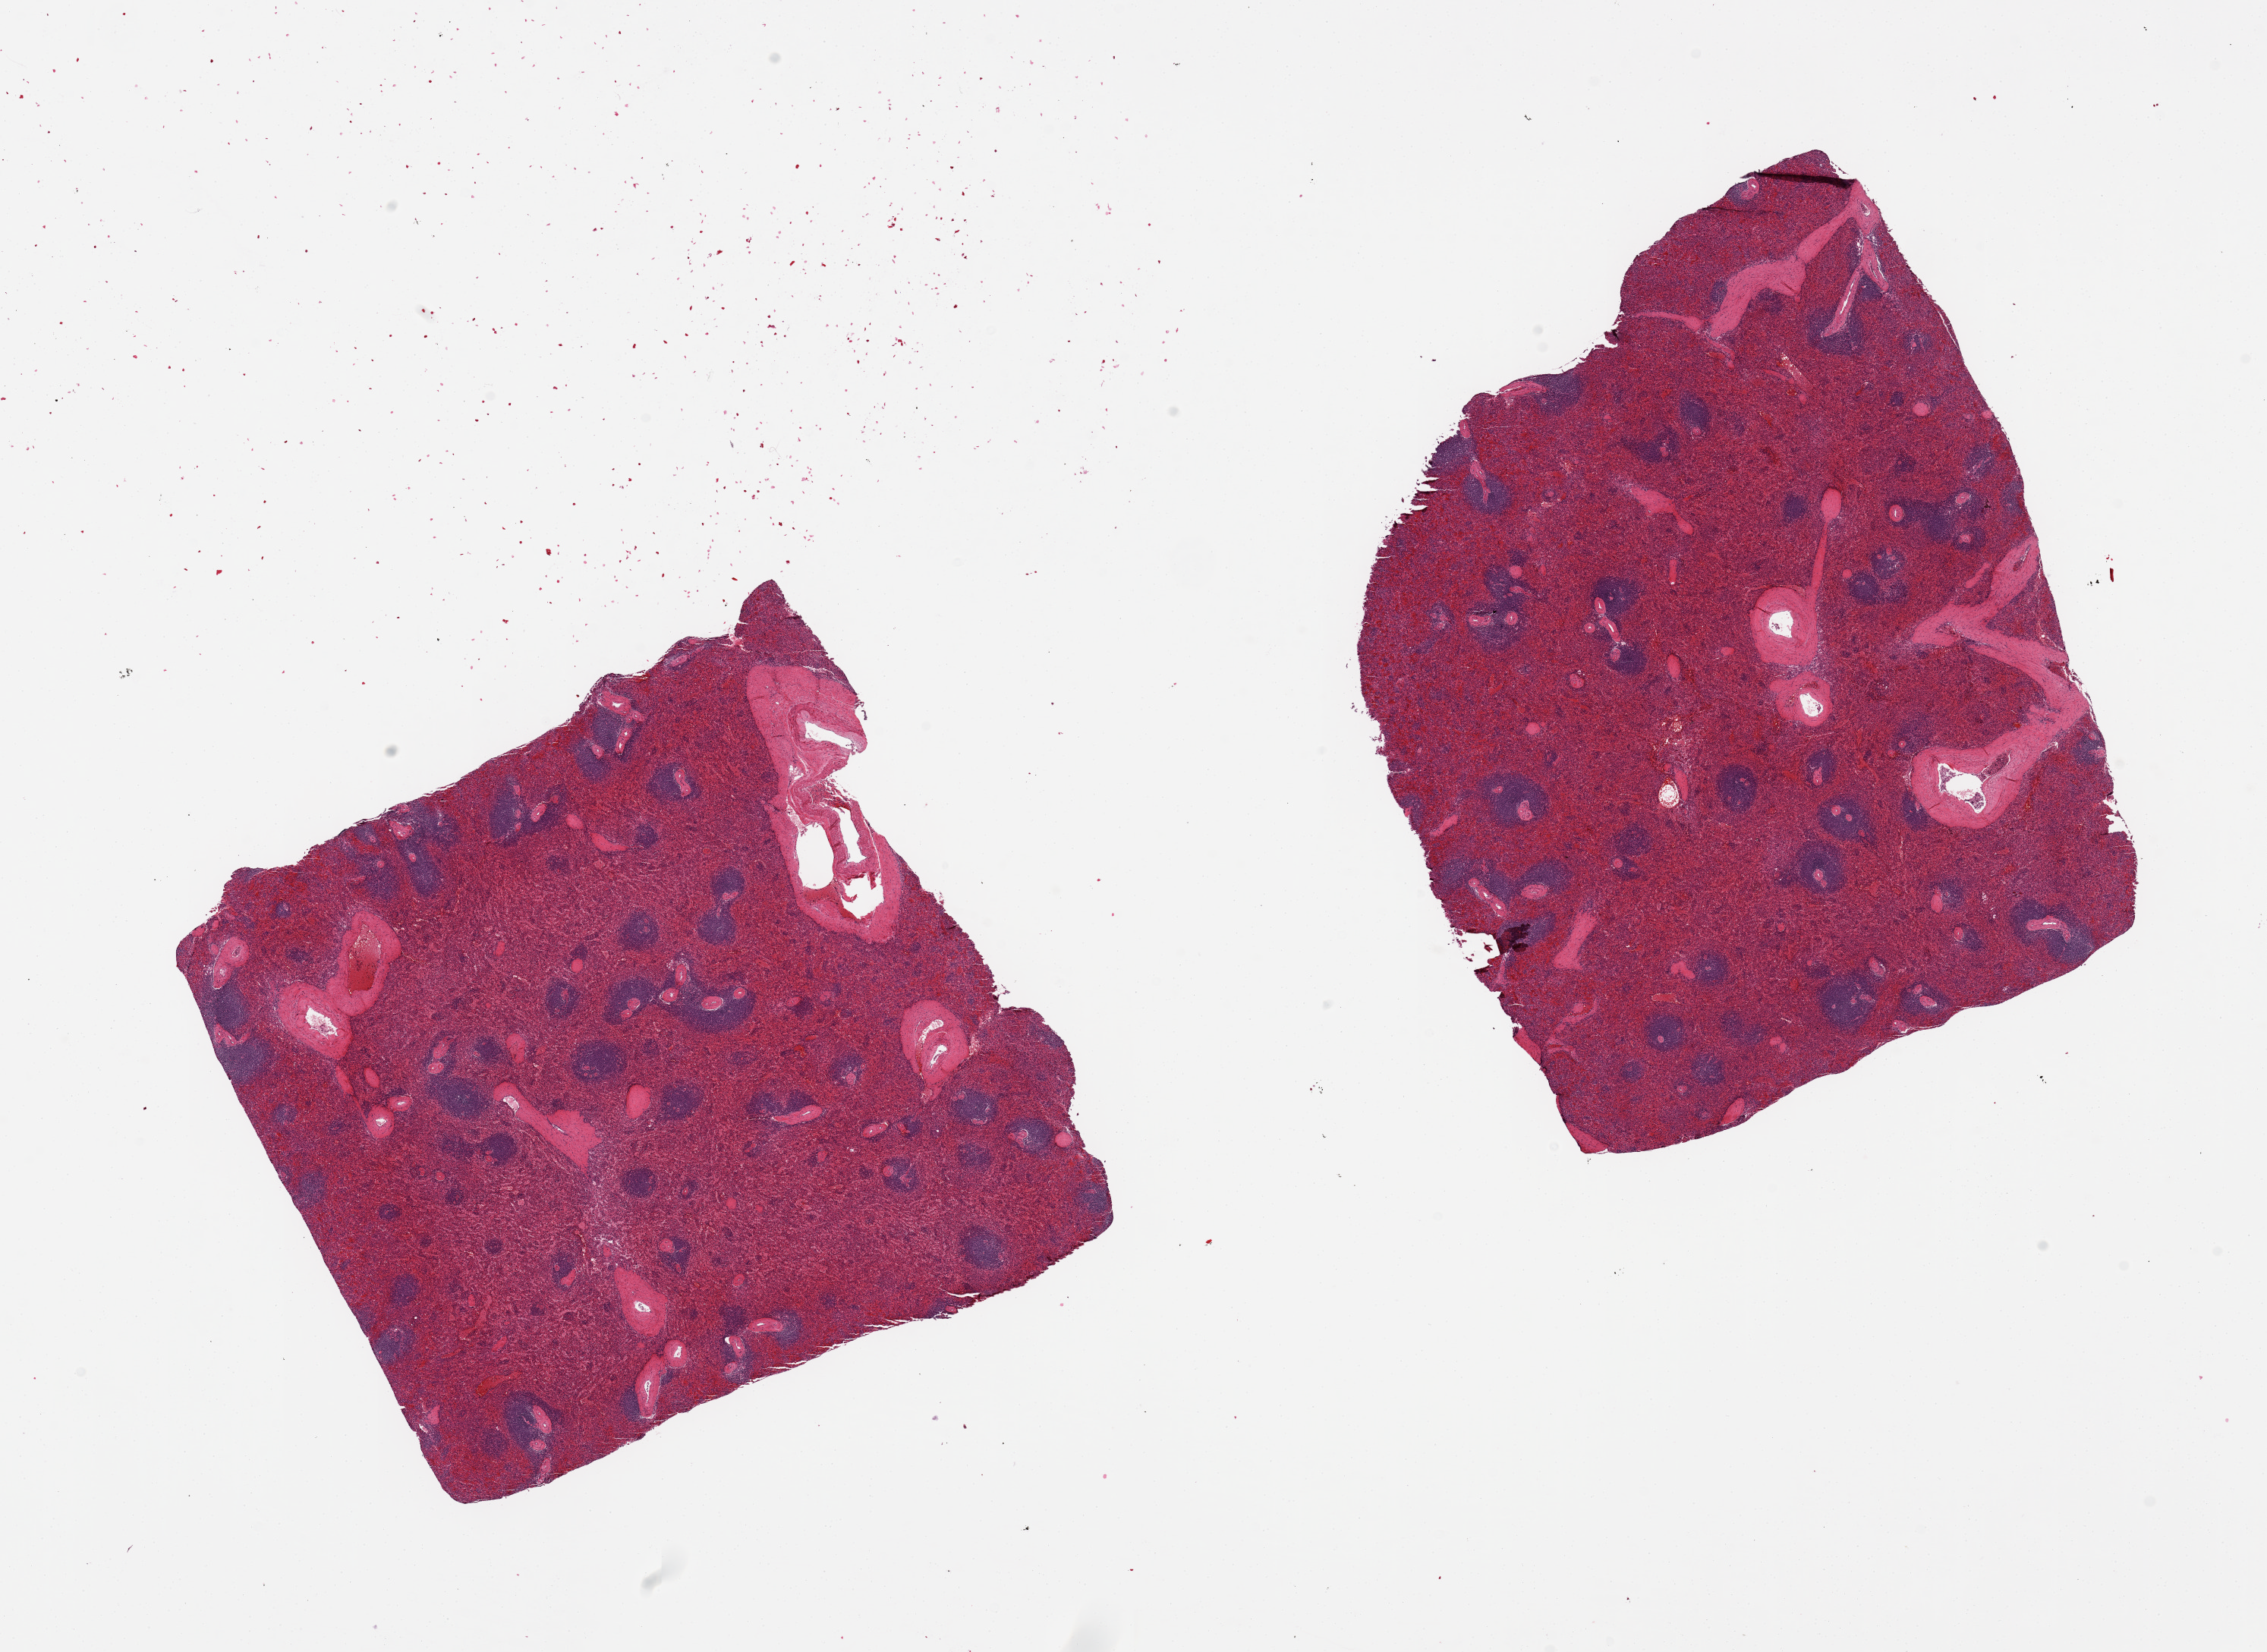
Digitized H&E-stained section, shown as a low-resolution overview of the whole scanned area (about 23.6 x 17.2 mm, slide scanned at 20x). PAXgene-fixed, paraffin-embedded tissue. Target tissue: spleen. Donor tissue sample. Donor sex: male.
- pathologist's review note for this sample: 2 pieces, 8x8 & 9x7mm; moderate congestion